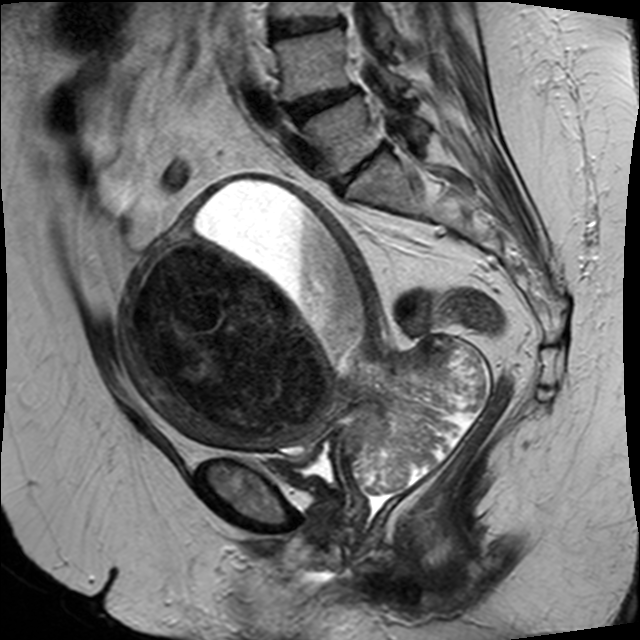
Pelvic MRI for cervical cancer, one sagittal slice. Slice 16 of 34 in the series (ordered by position). T2-weighted. 1.5 T. TE 89 ms, TR 3320 ms. 640 × 640 image matrix, field of view 260 × 260 mm. Female patient, age 50 years.
Outlined on this slice (outlined manually by an expert reader):
- uterus and cervix: bounding box [x1, y1, x2, y2] px = [119, 171, 485, 493]